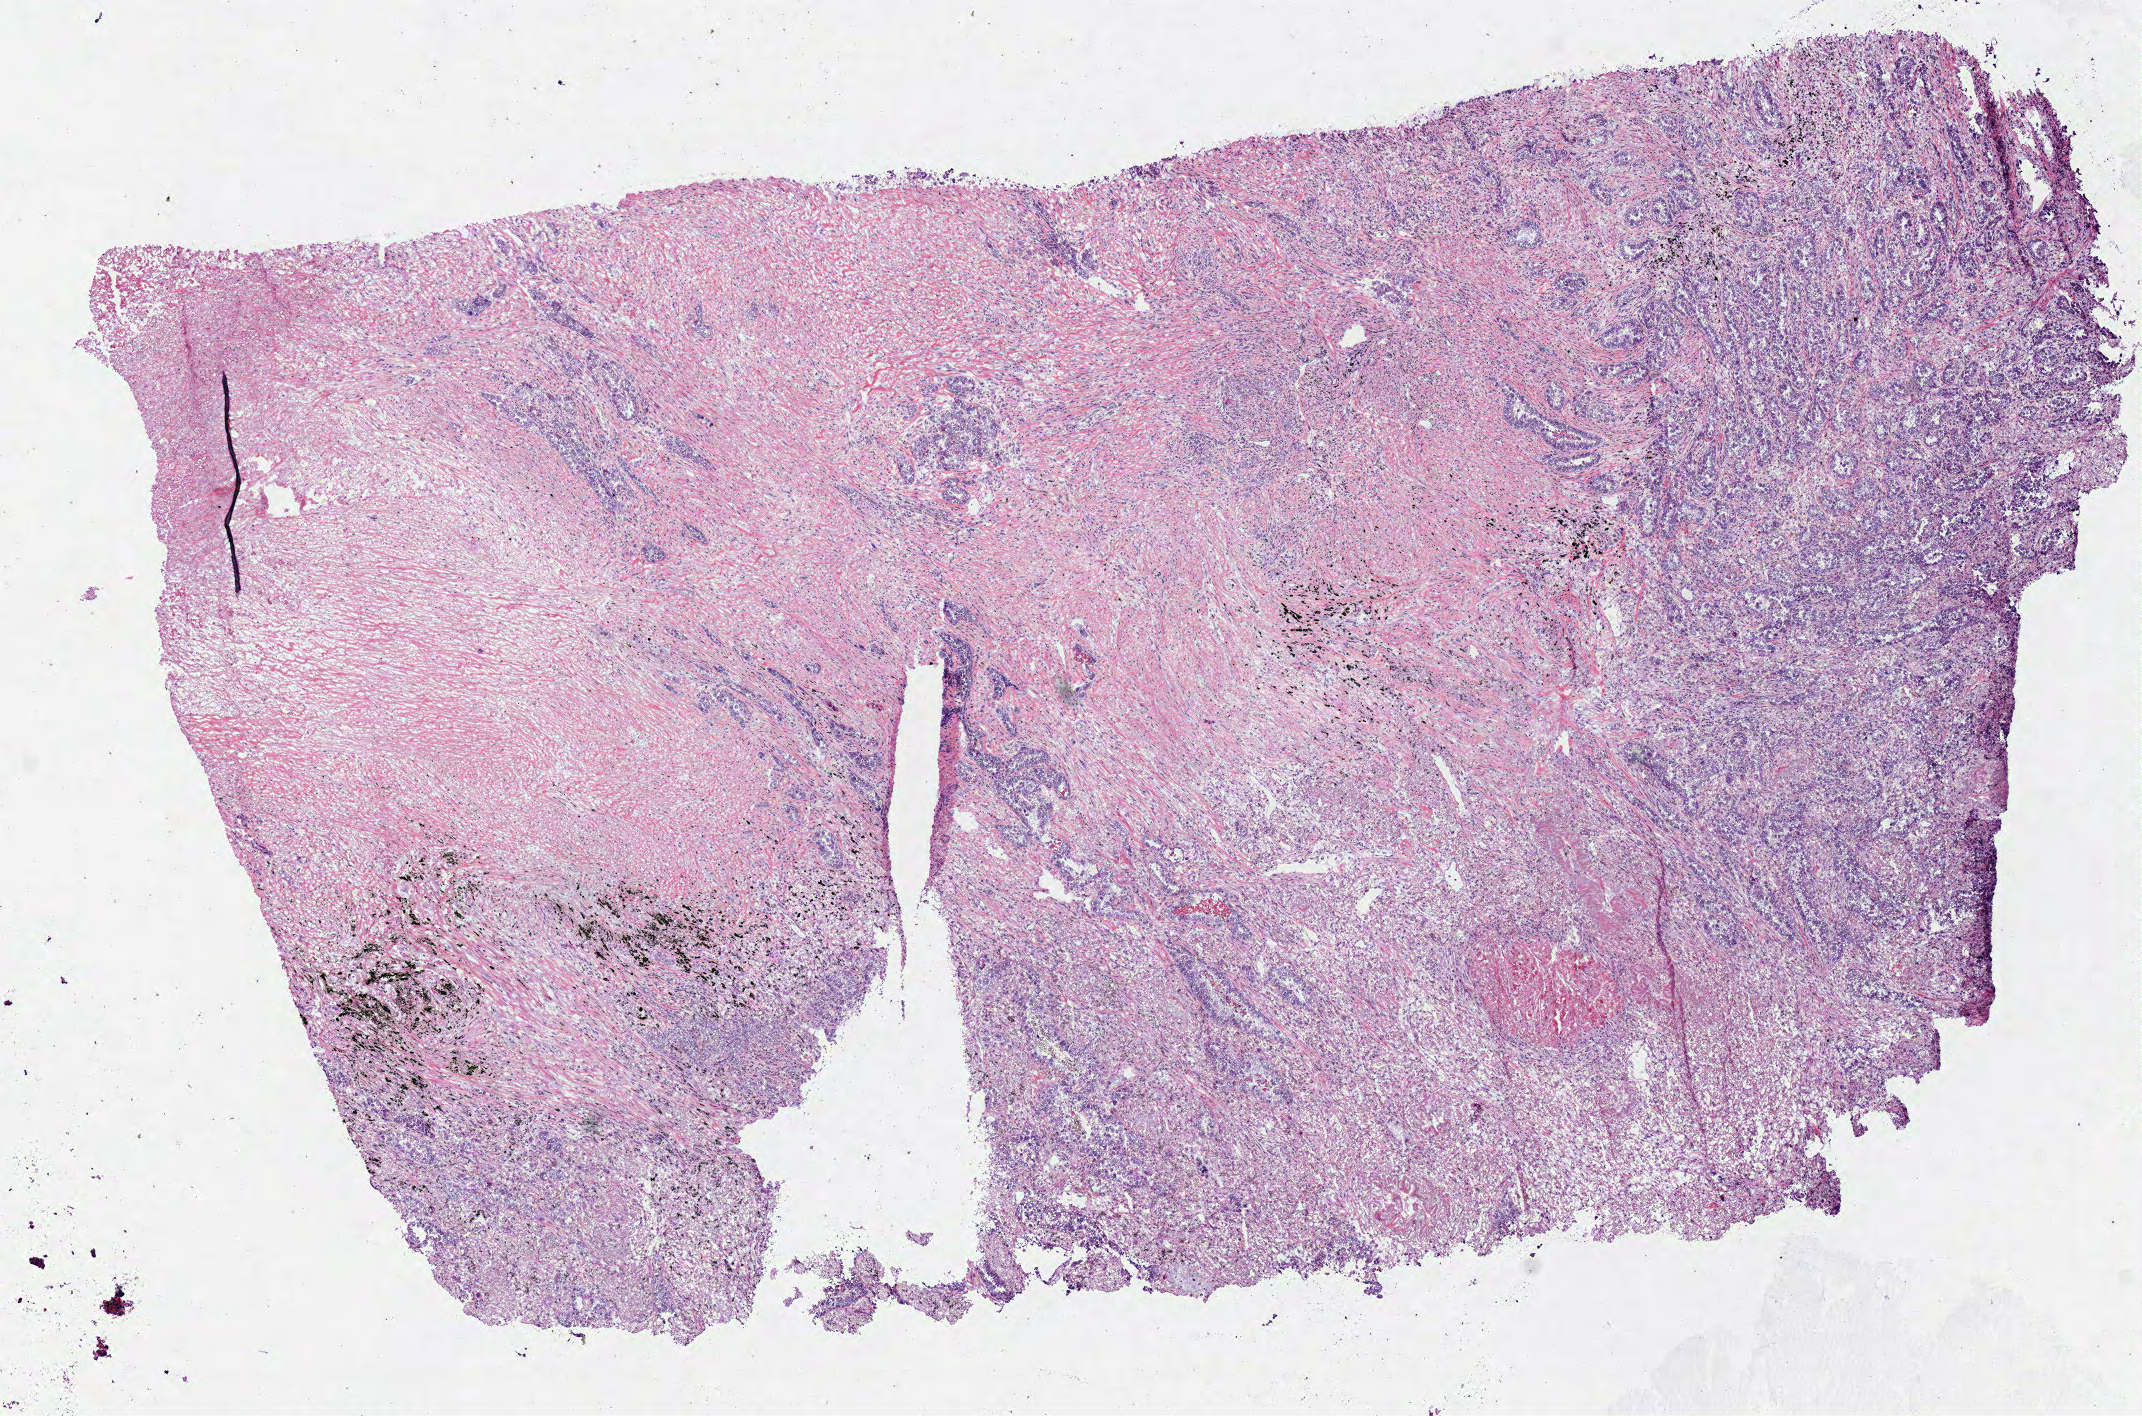
Hematoxylin and eosin (H&E) stained whole-slide image — a low-resolution overview of the entire scanned area, about 8.4 x 5.6 mm (acquisition: 40x scan), frozen section, lung, primary tumour sample. Male patient; age at initial diagnosis 78 years. Pathologist review of this section (percent, as recorded): tumour cells 45%, tumour nuclei 75%, normal cells 0%, stromal cells 50%, necrosis 5%.
* diagnosis: Bronchiolo-alveolar carcinoma, non-mucinous (lower lobe, lung)
* AJCC pathologic stage: IB (5th edition)
* laterality: right